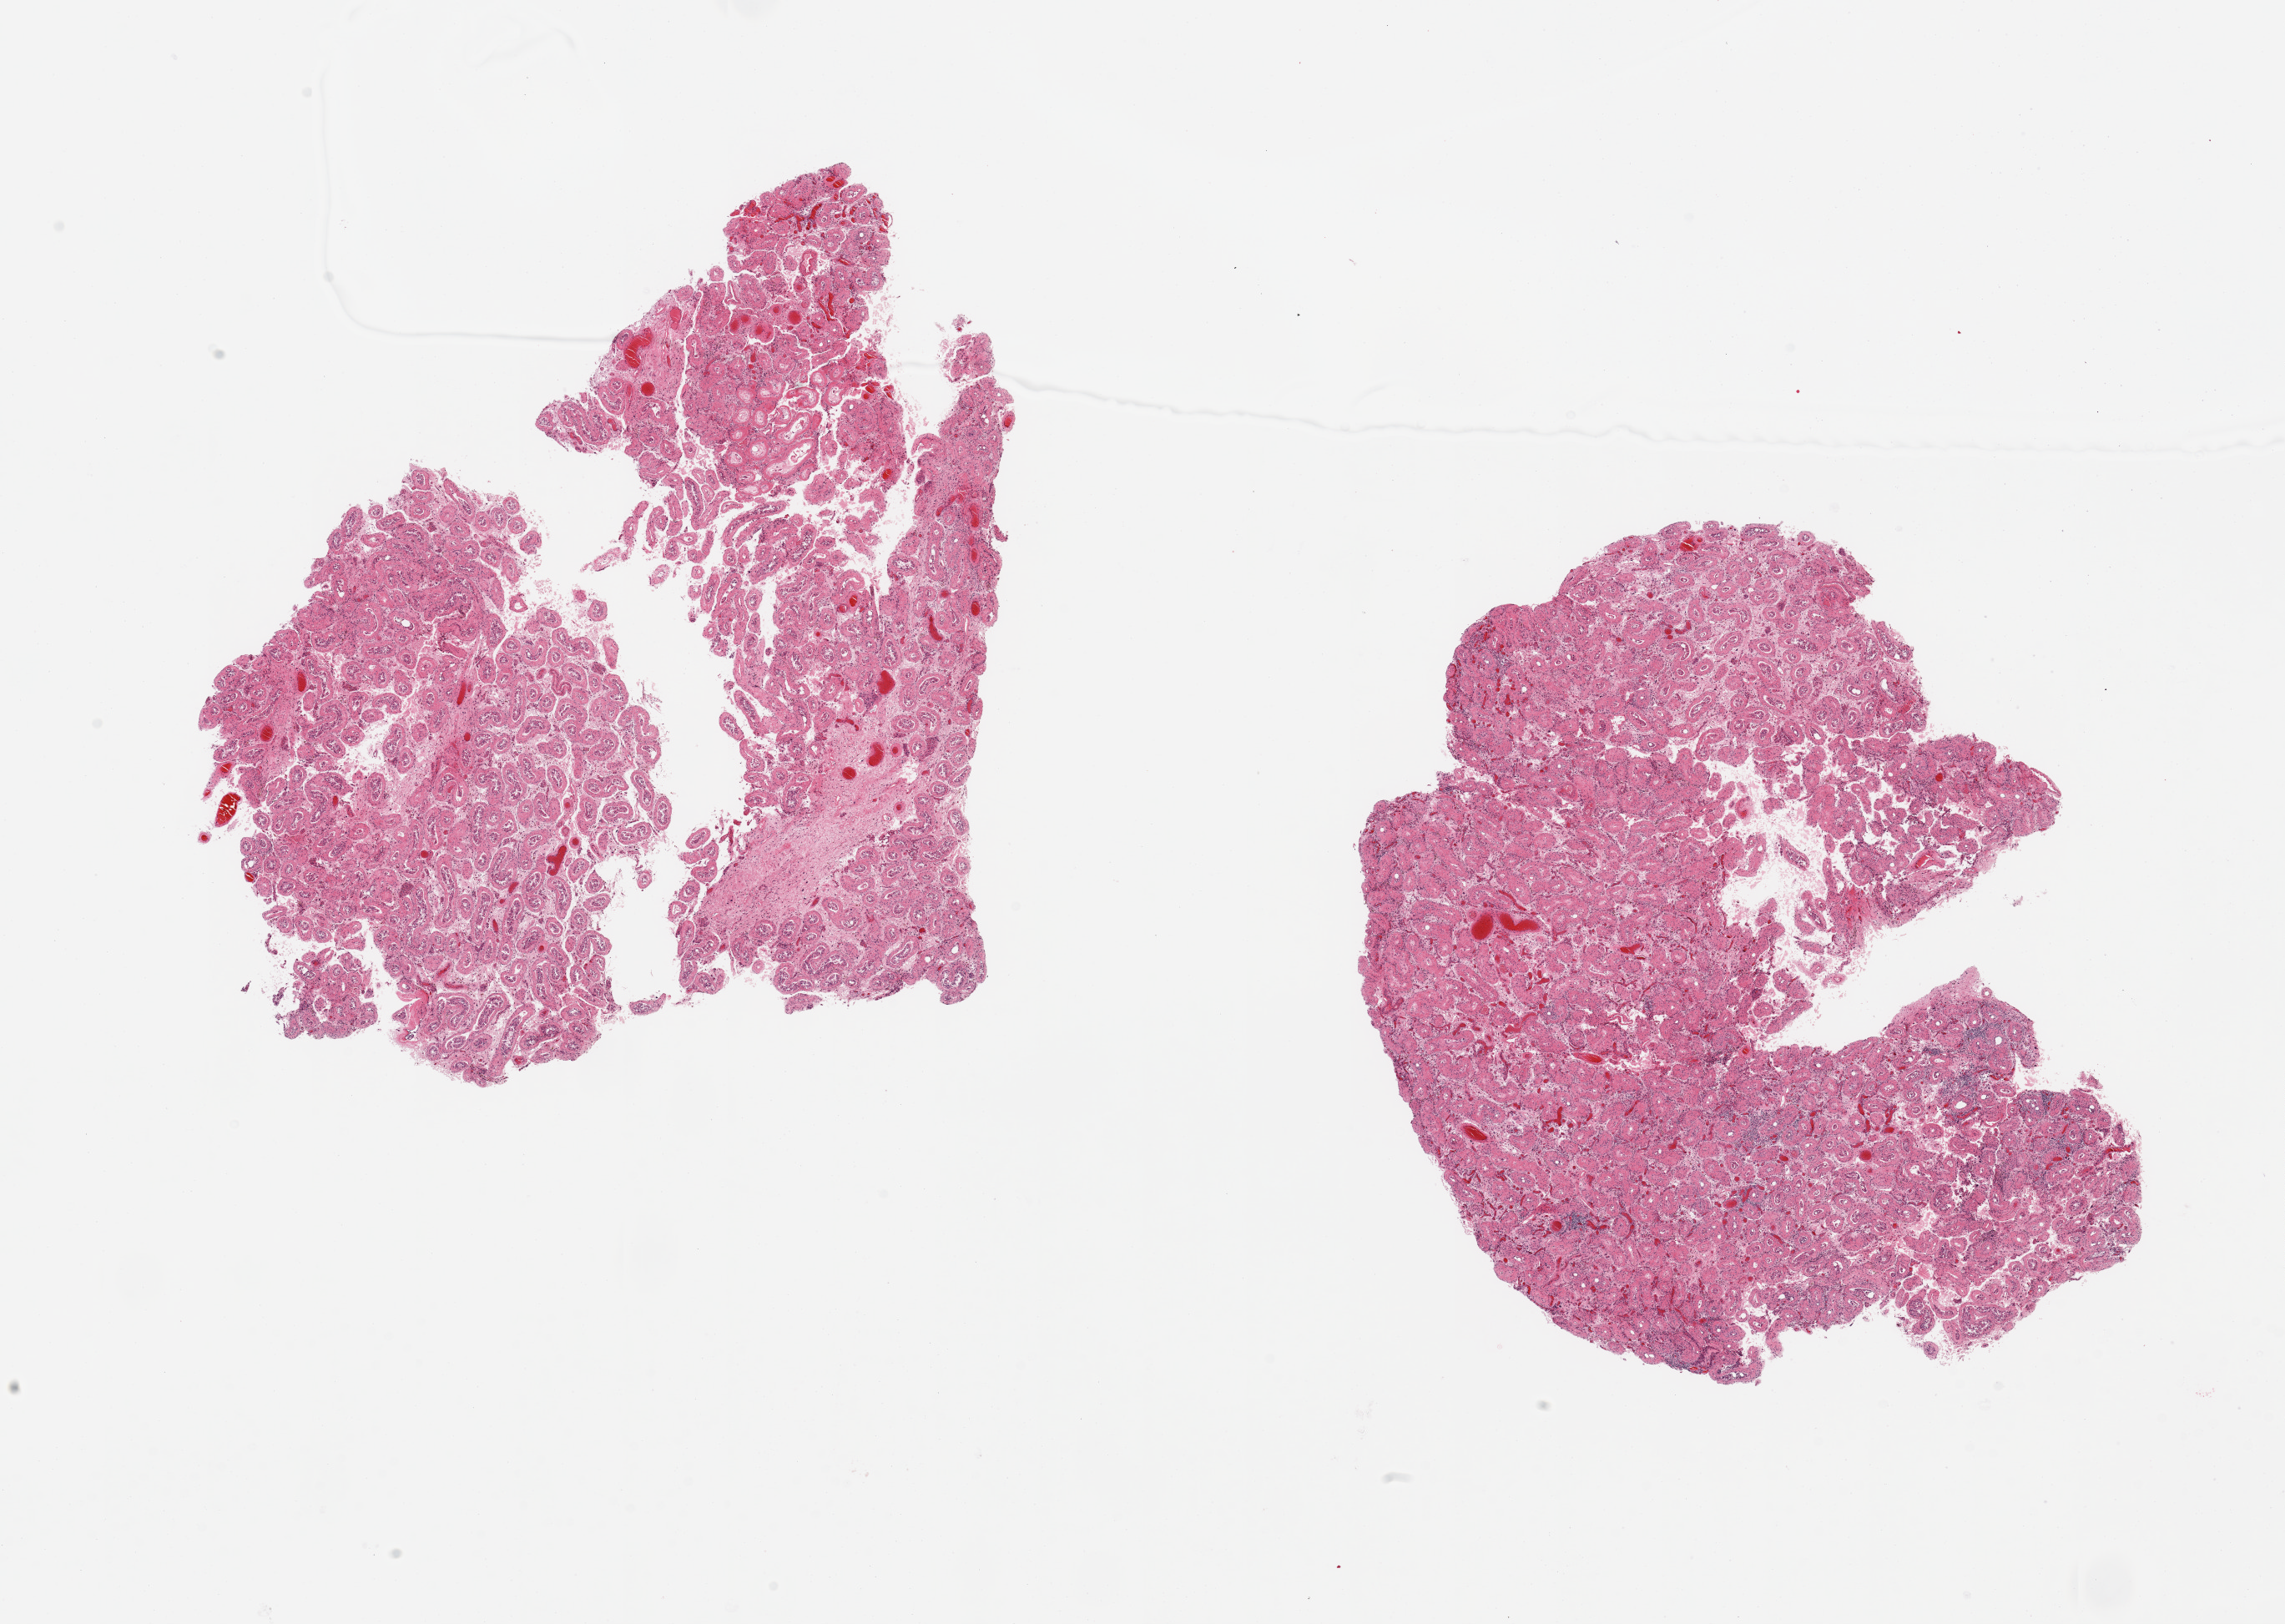
Hematoxylin and eosin (H&E) whole-slide image, brightfield — low-resolution overview of the scanned area, about 21.7 x 15.4 mm (acquisition: 20x scan). PAXgene-fixed paraffin-embedded (PFPE) section. Target tissue: testis. Donor tissue sample. Donor sex: male.
• review note (as recorded): 2 pieces, diffuse tubular atrophy/sclerosis